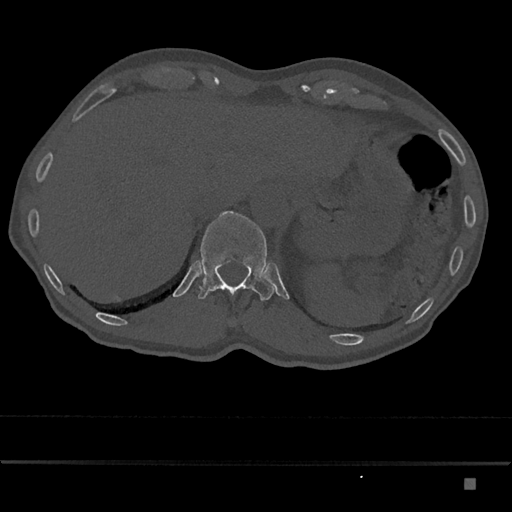
CT including the spine, one axial slice. Position 620 of 797 along the scan axis. Bone window (W 1800 / L 400 HU). 0.5 mm slice thickness. 512 × 512 image matrix, field of view 390 × 390 mm. Male patient, age 72 years. From the clinical record (not read from this slice): primary cancer: prostate.
Outlined on this slice (semi-automatically segmented with operator editing):
- T12 vertebra: bounding box [x1, y1, x2, y2] px = [198, 211, 276, 301]